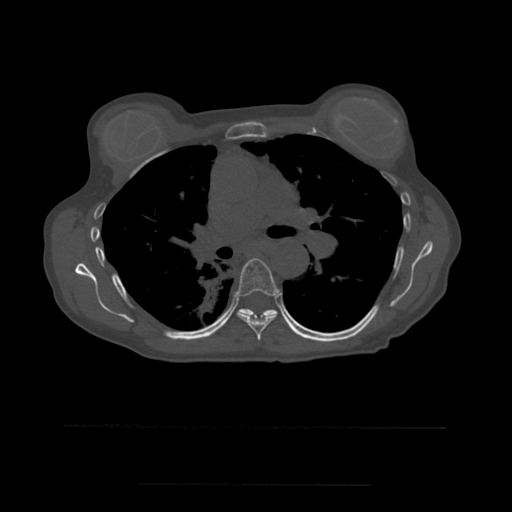
CT including the spine, one axial slice. Position 371 of 544 along the scan axis. Bone window (W 1800 / L 400 HU). 512 × 512 image matrix, field of view 350 × 350 mm. Patient age 58 years. Case-level facts recorded for this patient, not image findings: primary cancer: lung.
Annotated regions visible in this slice (semi-automatically segmented with operator editing):
- T6 vertebra: bounding box (x1, y1, x2, y2) in pixels: (235, 258, 281, 341)
- T7 vertebra: (240, 309, 290, 327)